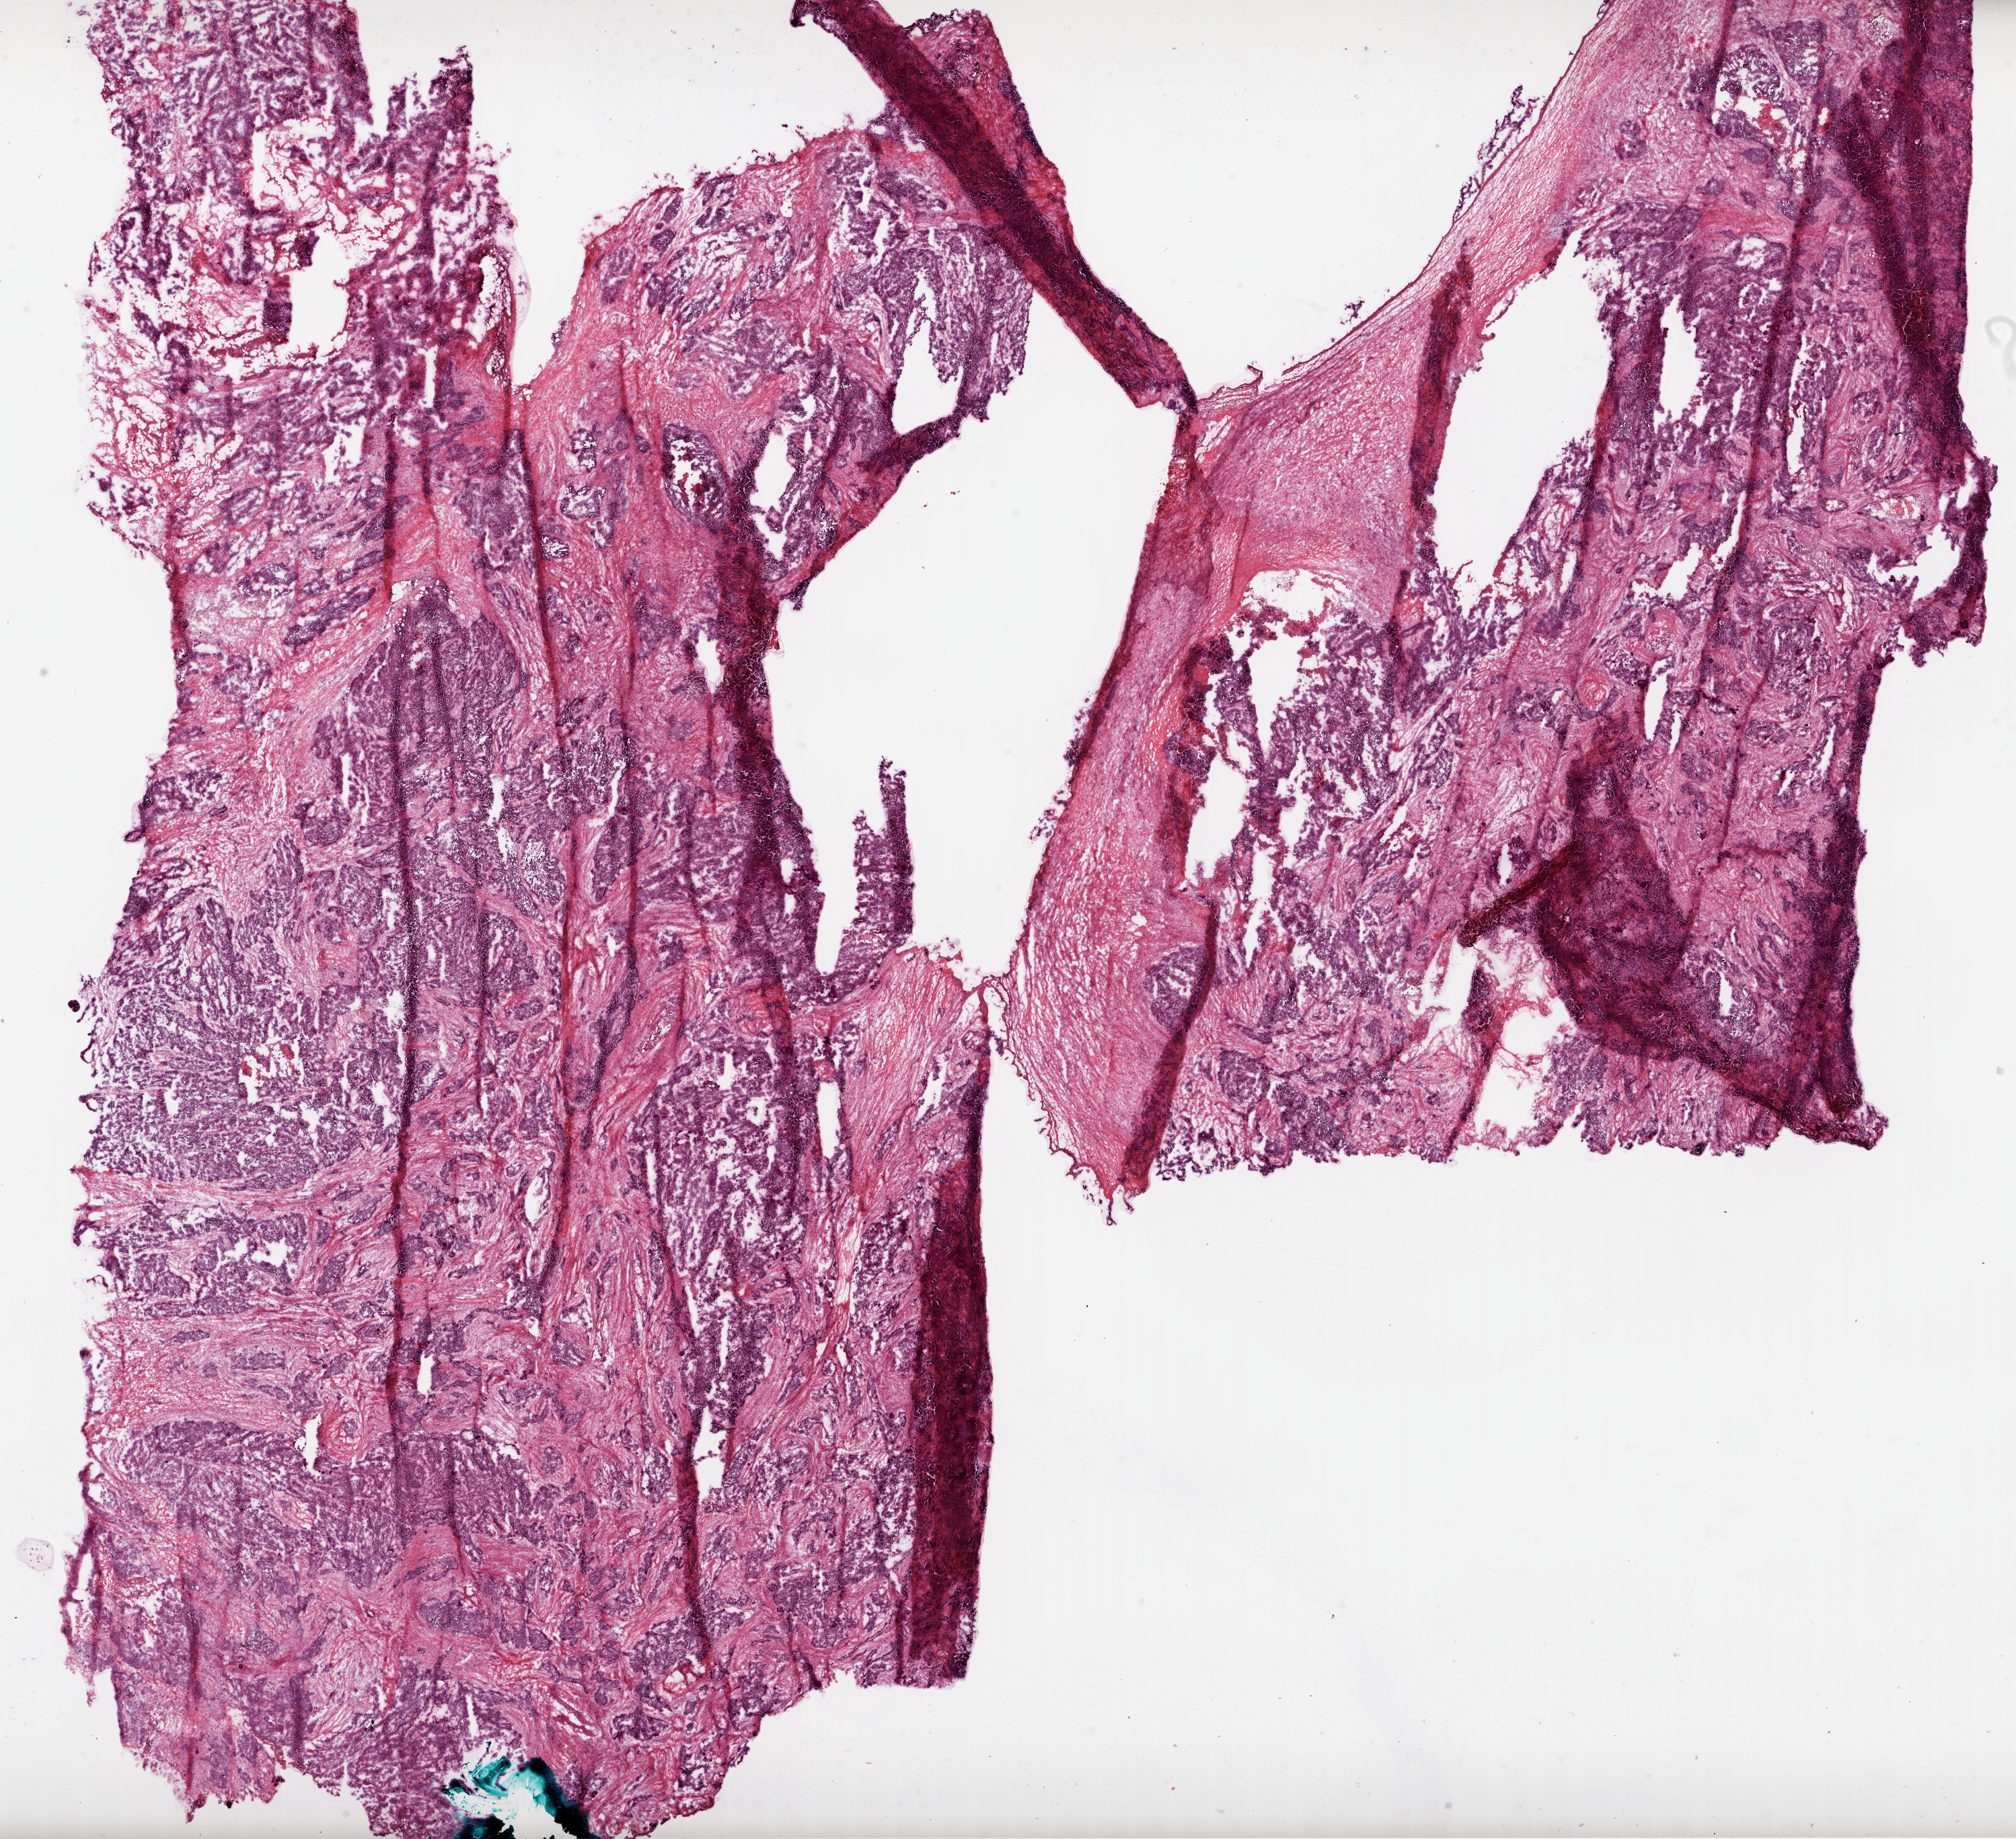
Hematoxylin and eosin (H&E) stained whole-slide image, a low-resolution overview of the entire scanned area, about 24.2 x 22.1 mm; frozen section from the bottom of the tissue portion; ovary, primary tumour sample. Female, age 65 years at initial diagnosis. Histologic grade: G3 (poorly differentiated). Slide review estimates, as recorded: tumour cells 70%, tumour nuclei 95%, normal cells 0%, stromal cells 30%, necrosis 0%.
Histologic diagnosis: Serous cystadenocarcinoma, NOS. FIGO stage: IIIC.